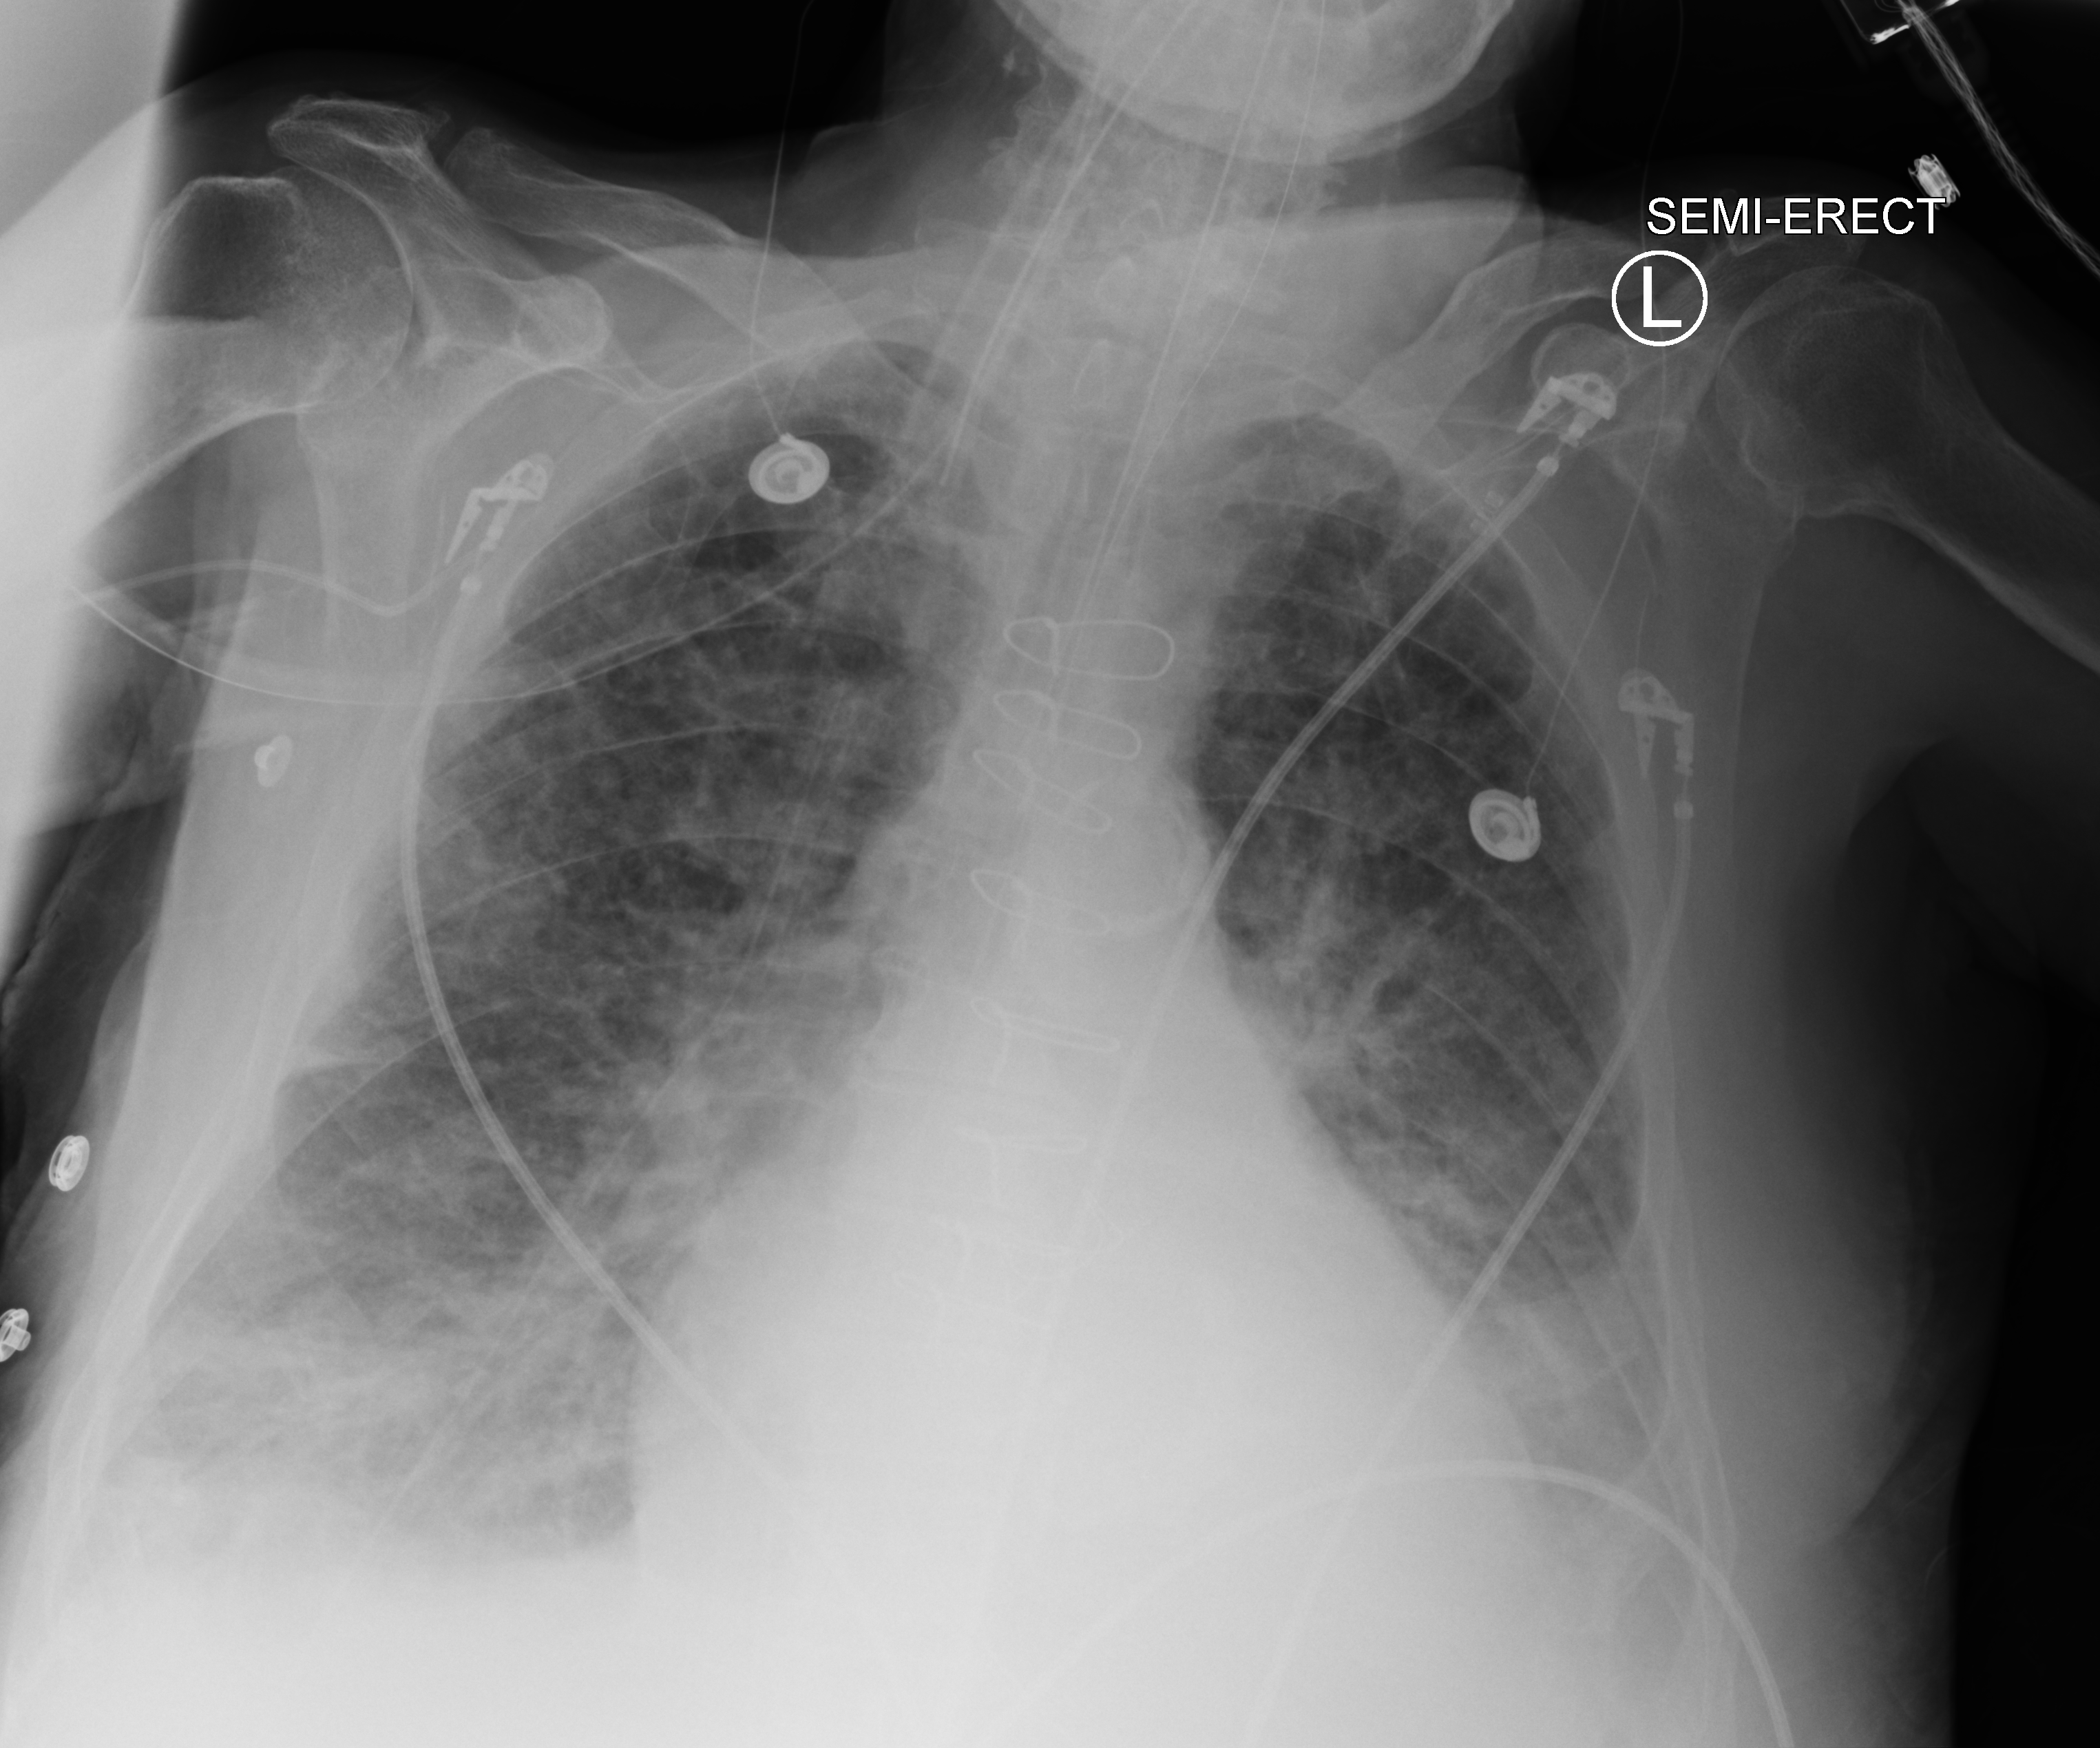
Chest X-ray (portable), anteroposterior (AP) projection. Patient hospitalised with COVID-19; male, aged 75–90 years.
Admission-level facts for this patient (not findings on this image; timing relative to this image not recorded):
- admitted to intensive care during this hospital stay: yes
- mechanically ventilated during this hospital stay: yes